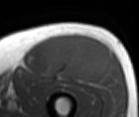
MRI of an extremity soft-tissue mass, one axial slice. Slice 47 of 86 in the series (ordered by position). MR volume resampled by the dataset authors to the PET/CT grid (not the native acquisition matrix). 3.27 mm slice thickness. 139 × 117 image matrix, field of view 136 × 114 mm. Male patient. Case-level facts recorded for this patient, not image findings: histological type: extraskeletal osteosarcoma; grade: high; site of the primary tumour: thigh.
Annotated regions visible in this slice (expert contour drawn on MRI and transferred to this co-registered scan by the dataset authors):
- gross tumour volume (mass): bounding box <45,34,108,81> (left, top, right, bottom; pixels)